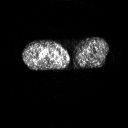
FDG PET of an extremity soft-tissue mass (from a PET/CT study), one axial slice; slice 237 of 311 in the series (ordered by position); 3.27 mm slice thickness; 128 × 128 image matrix, field of view 700 × 700 mm. Male patient, age 50 years. From the clinical record (not read from this slice): histological type: undifferentiated - pleiomorphic; grade: high; site of the primary tumour: right thigh.
Structures marked on this image (expert contour drawn on MRI and transferred to this co-registered scan by the dataset authors):
- gross tumour volume including surrounding oedema: bounding box <42,51,55,59> (left, top, right, bottom; pixels)